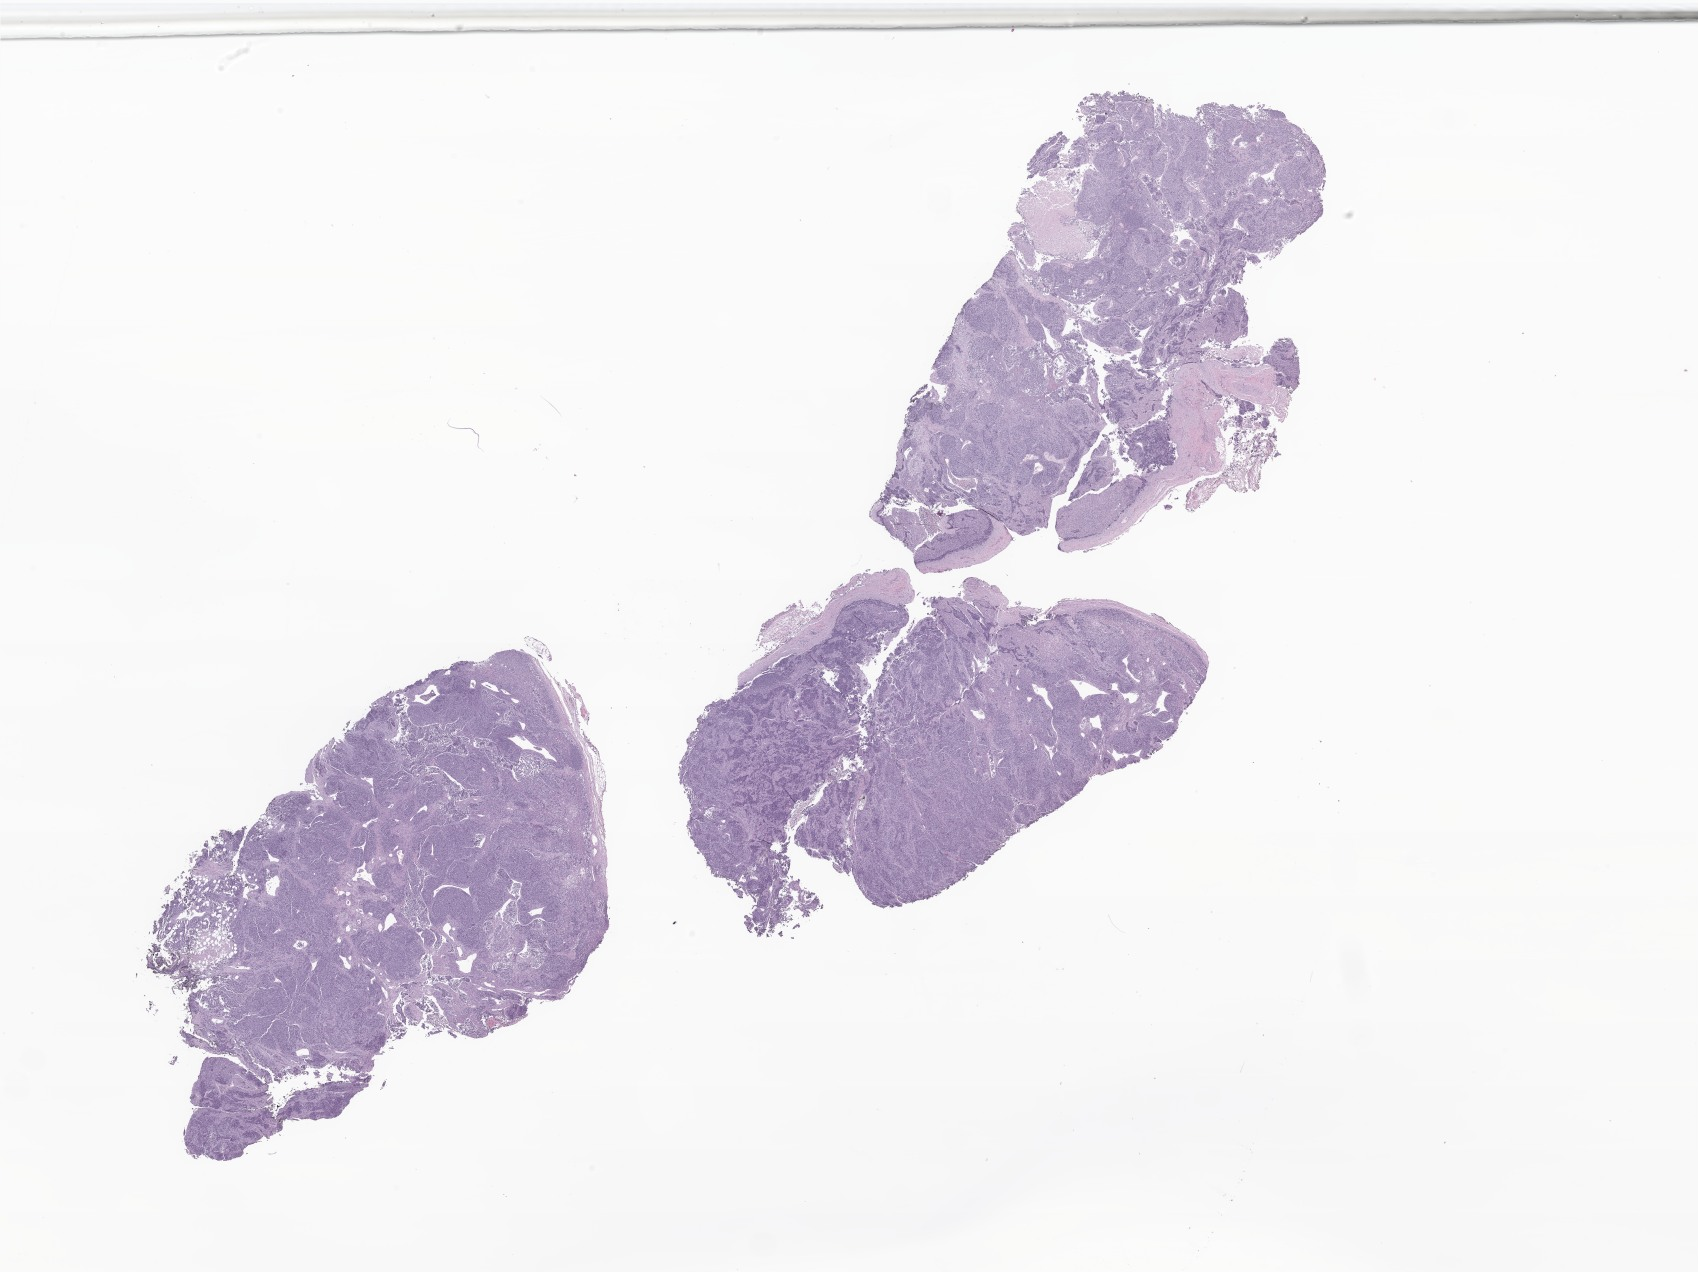
Whole-slide image, hematoxylin and eosin (H&E) stain of tumor tissue from the soft tissue of upper extremity — whole scanned area (about 28.6 x 21.5 mm) shown as a low-resolution overview, formalin-fixed, paraffin-embedded (FFPE) tissue. Patient: female, age 79 months (6 years 7 months).
• diagnosis: Rhabdomyosarcoma, NOS
• tissue or organ of origin (case record): connective, subcutaneous and other soft tissues of upper limb and shoulder